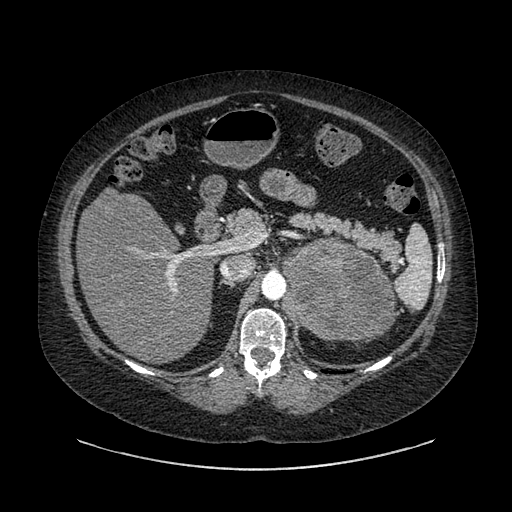
Contrast-enhanced abdominal CT, one axial slice; slice 571 of 769 in the series (ordered by position); reconstruction kernel SOFT; intravenous contrast given; soft-tissue window (W 400 / L 40 HU); 0.62 mm slice thickness; 512 × 512 image matrix, field of view 460 × 460 mm. Patient: female, 61 years. Case-level facts recorded for this patient, not image findings: diagnosis: adrenocortical carcinoma; tumour side: left adrenal; tumour size at pathology: 13 cm; Ki-67 index: 79 %; stage (as recorded): 2.
Structures marked on this image (semi-automatic segmentation, software-assisted and operator-edited):
- mass: box from (x=283, y=238) to (x=393, y=342) px